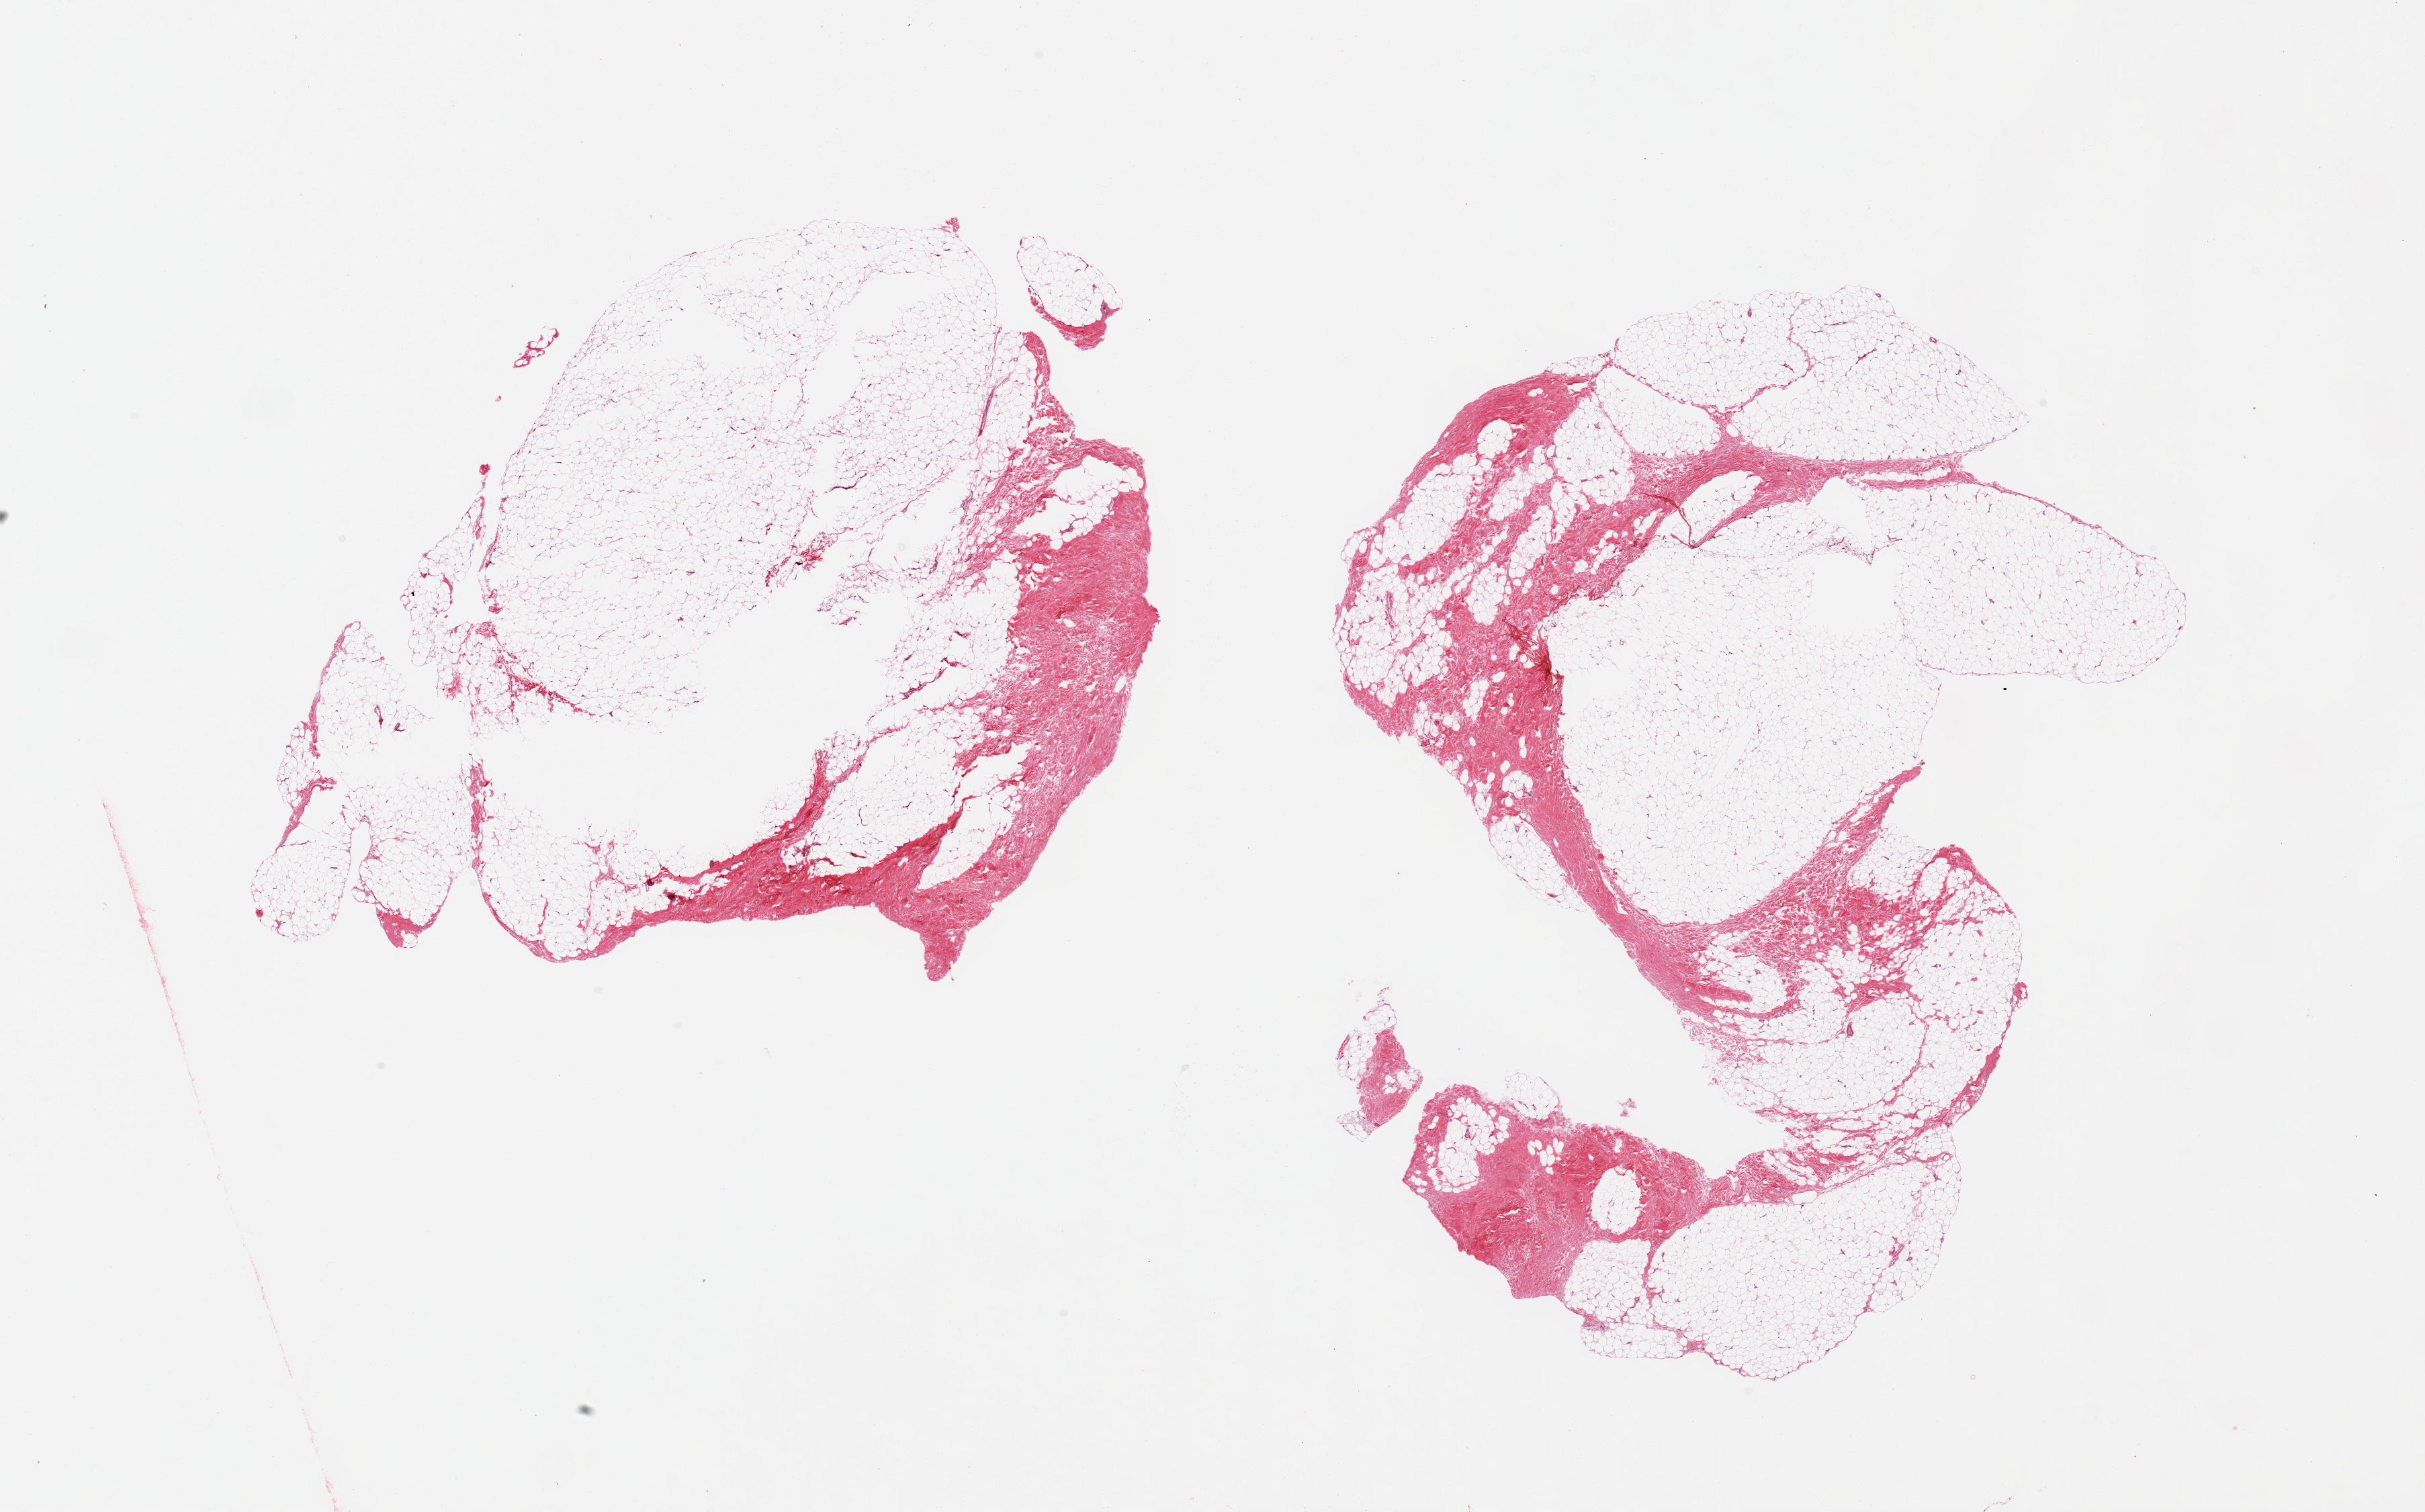
Digitized H&E-stained section, low-resolution overview of the scanned area, about 28.5 x 17.8 mm (slide scanned at 20x), PAXgene-fixed, paraffin-embedded tissue, sampled site (target tissue): breast, donor tissue sample. Male donor.
Reviewer comment on this tissue sample: 2 pieces, fibroadipose elements only.